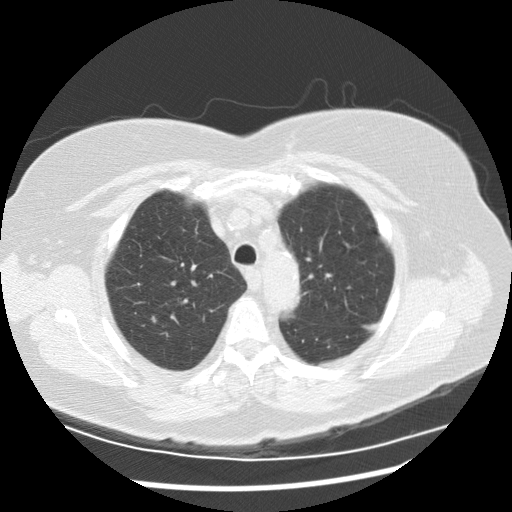
Chest CT (low-dose screening protocol), one axial image; second annual screen; lung window (W 1500 / L -600 HU); 2.5 mm slice thickness; standard (soft-tissue) reconstruction kernel (STANDARD); slice 48 of 225 in the series; 512 × 512 image matrix. Female participant, aged 72 years at enrolment. Current smoker at enrolment.
Lesion marked by an expert reader, bounding box [x1, y1, x2, y2] px = [129, 310, 166, 338]. No non-calcified nodule or mass ≥4 mm was recorded by the screening reader at this exam.